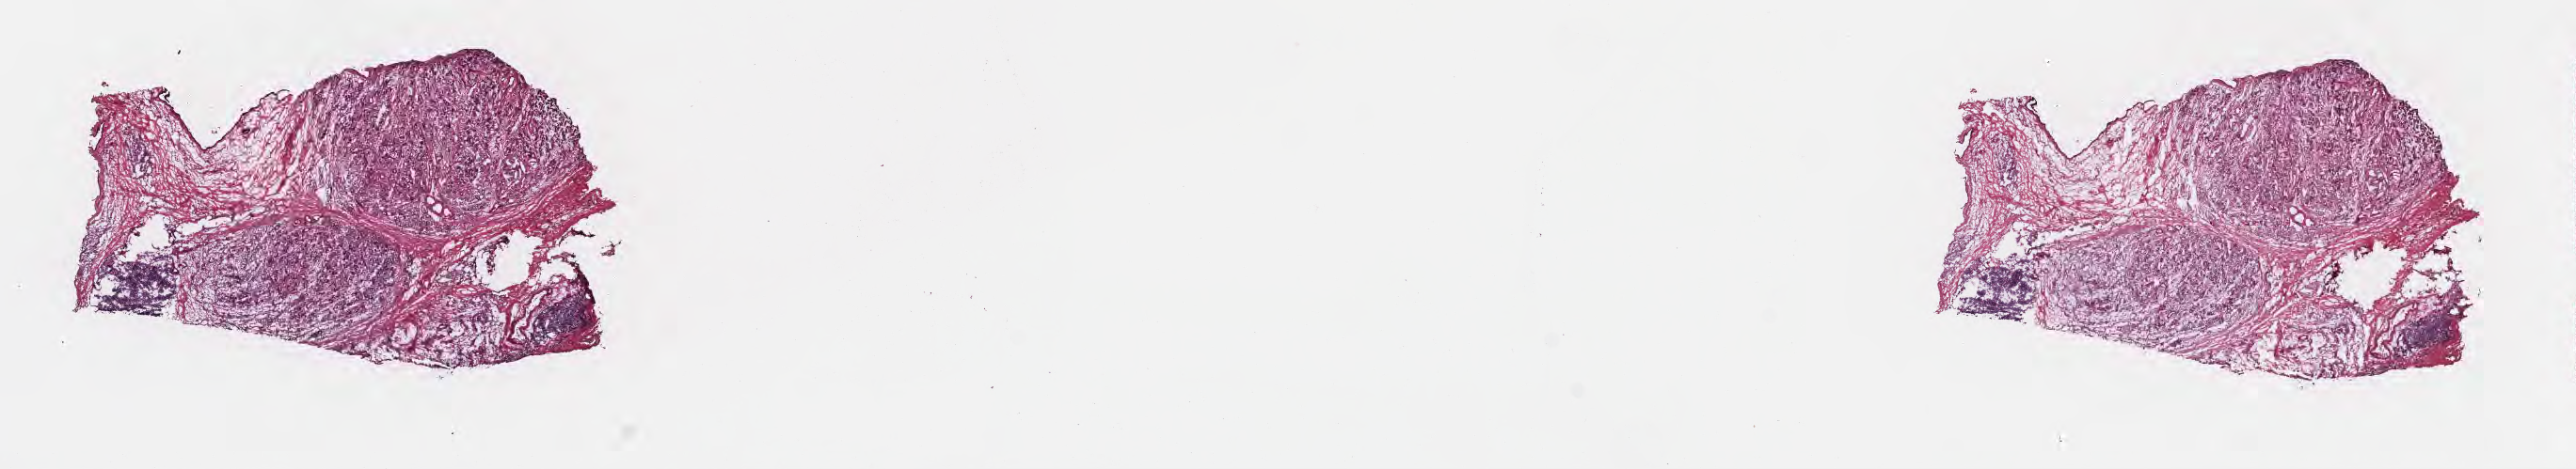
H&E whole-slide image, whole scanned area (about 22.1 x 4.0 mm) shown as a low-resolution overview. Frozen section (tissue freezing medium). Specimen: primary tumor. Anatomic site: head of pancreas. Male, age 75 years at initial diagnosis. Tumor grade: G3 (poorly differentiated). Pathologist review of this section (percent, as recorded): tumor cells 40%, tumor nuclei 50%, stromal cells 30%, necrosis 0%, normal cells 30%. Inflammatory infiltration, as recorded: lymphocyte infiltration 0%, monocyte infiltration 0%, neutrophil infiltration 0%.
AJCC pathologic stage: Stage III. Diagnosis: Infiltrating duct carcinoma, NOS. Section: top of the tissue portion.